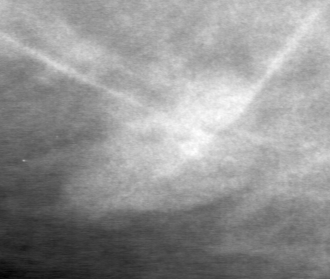
Region of interest cut from a scanned film mammogram (one marked finding), right breast, MLO view, BI-RADS breast density category 2 (scale 1–4).
Mass, shape oval, margins obscured; BI-RADS assessment category 0 (incomplete: needs additional imaging); subtlety rating 4 on a 1 (subtle) to 5 (obvious) scale; pathology result (as recorded, not read from the image): benign.